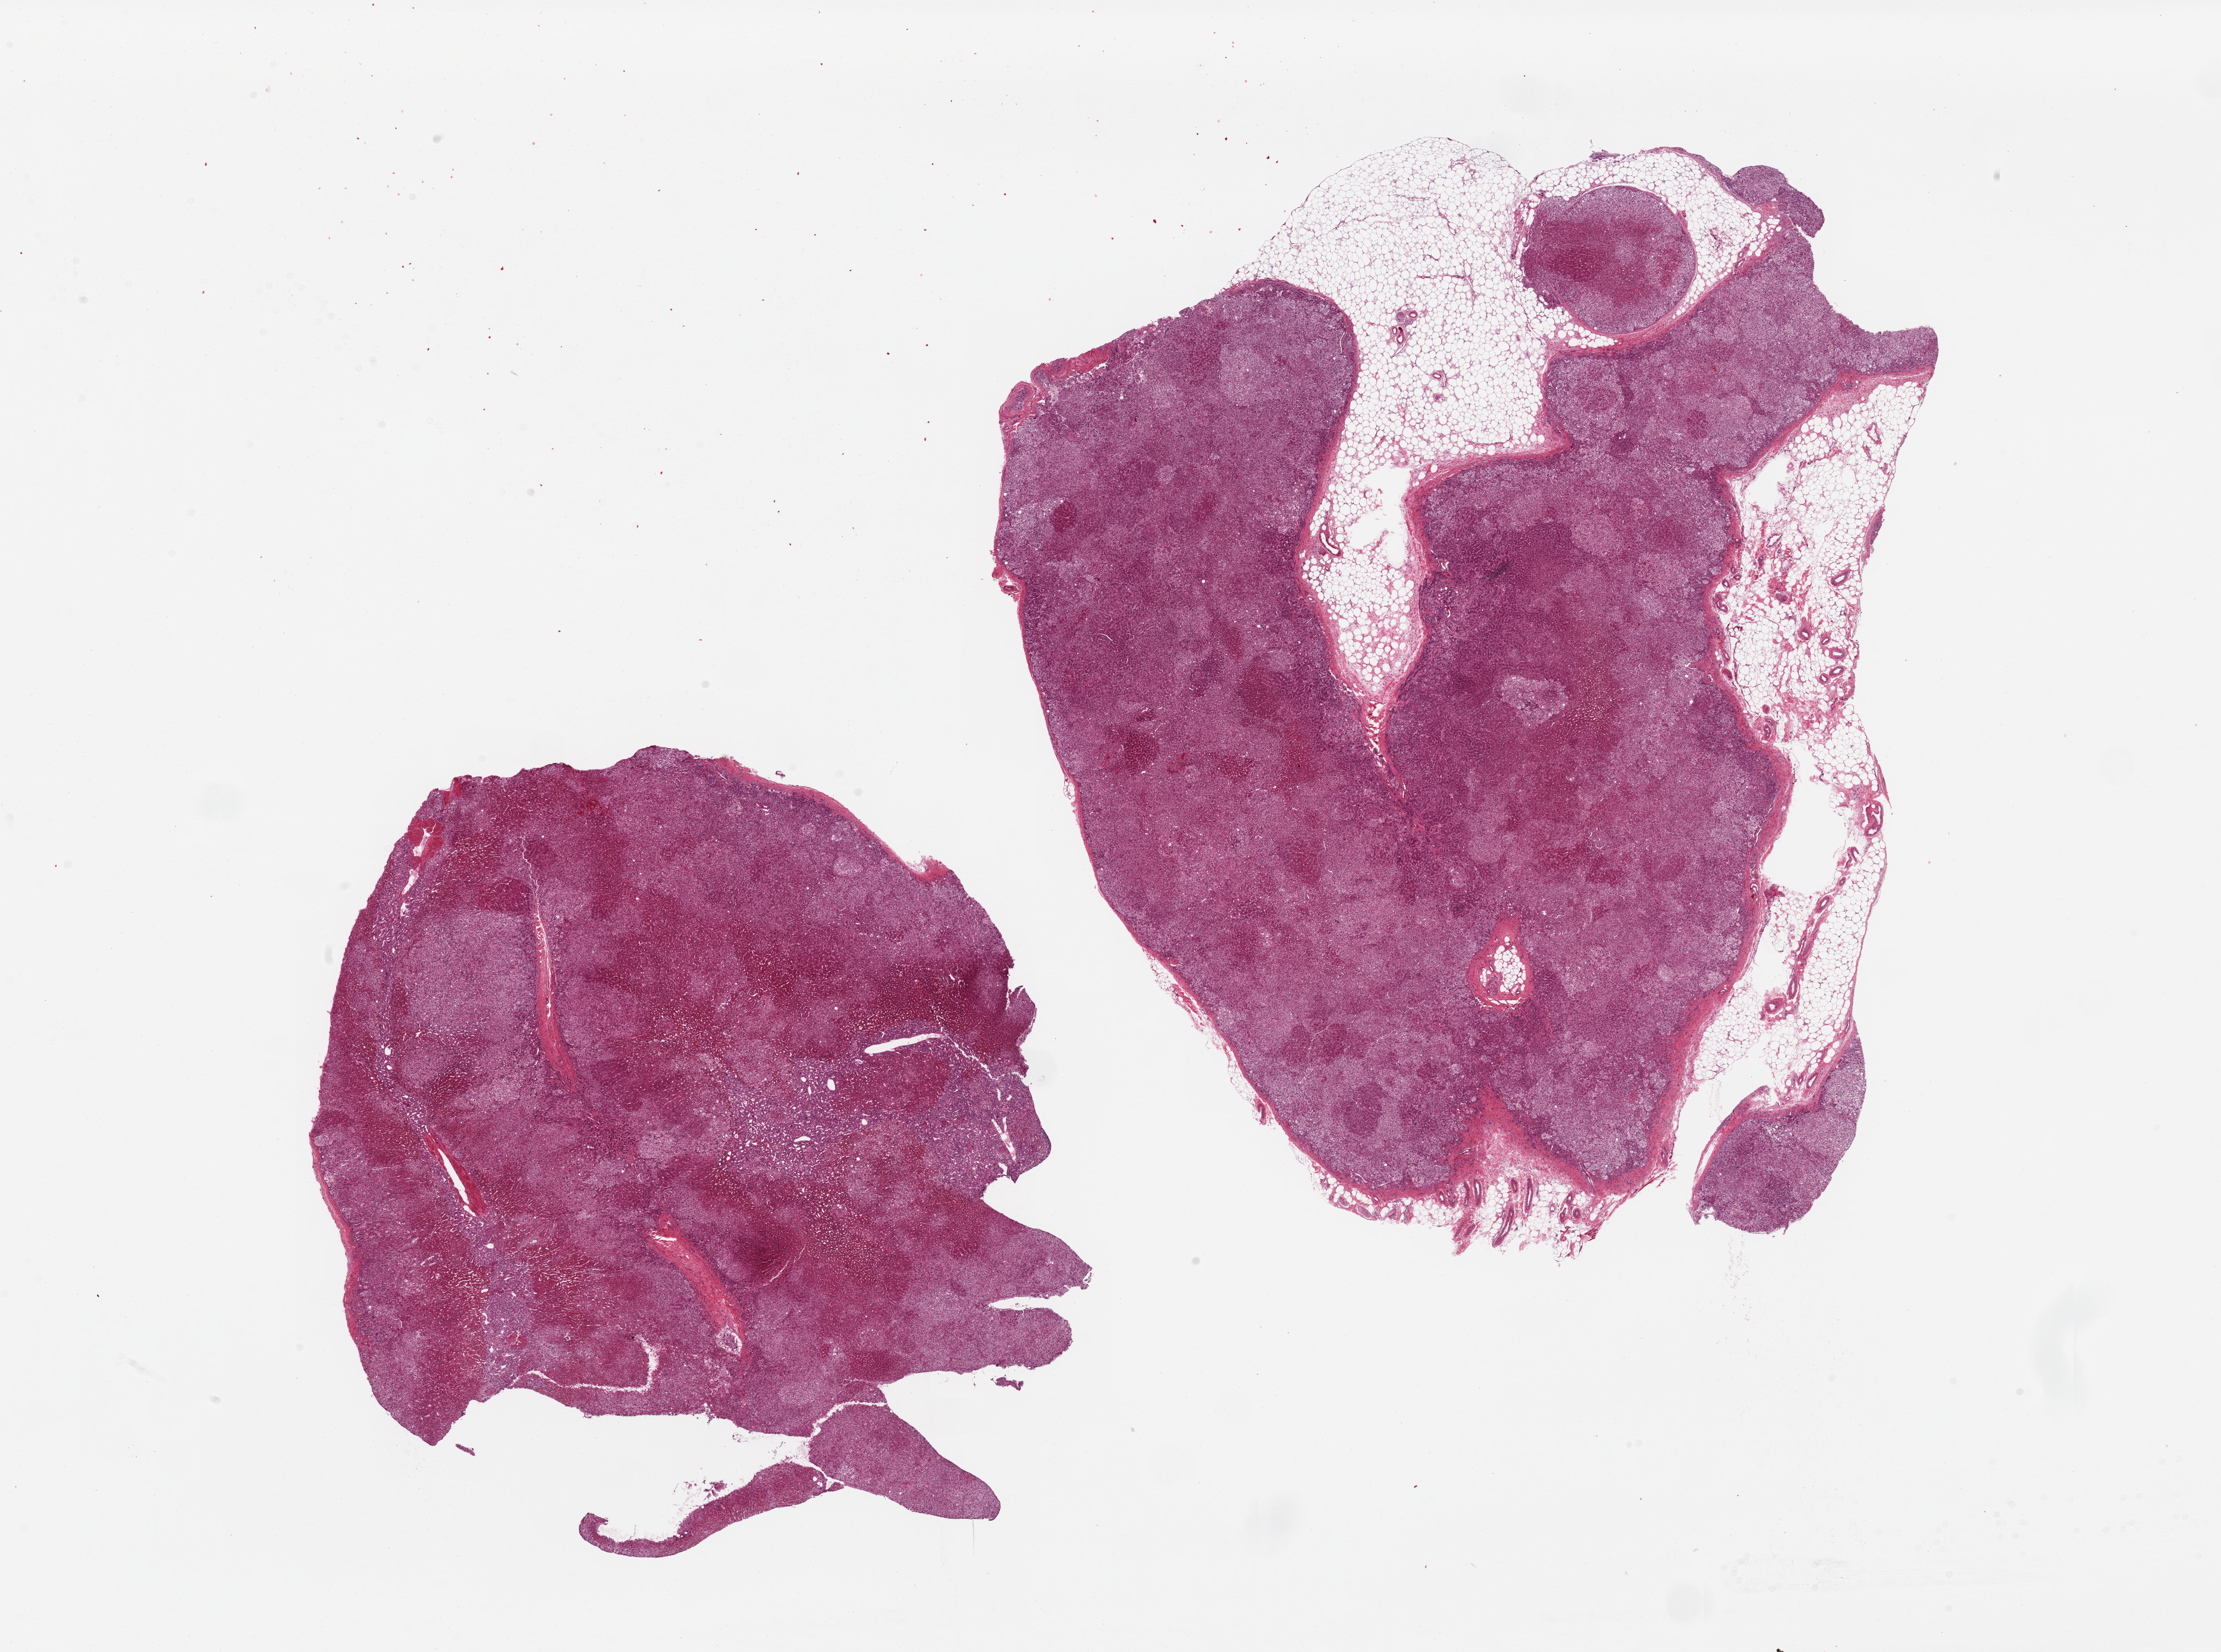
Hematoxylin and eosin (H&E) whole-slide image — low-resolution overview of the scanned area, about 29.5 x 22.0 mm; PAXgene-fixed, paraffin-embedded tissue; section of adrenal gland (target tissue); tissue donor sample. Male donor.
Pathologist's review note for this sample: 2 pieces, 12x10 and 15x13mm; 1 has 30% fat.